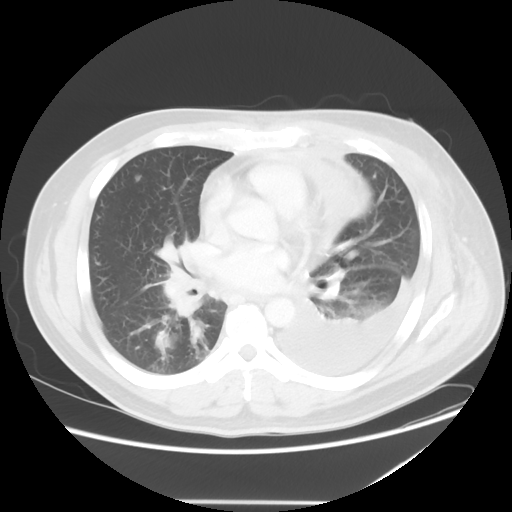
Chest CT, one axial slice. Slice 26 of 52 in the series (ordered by position). Reconstruction kernel STANDARD. 120 kVp. Lung window (W 1500 / L -600 HU). 5 mm slice thickness. 512 × 512 image matrix. Male patient, age 42 years. From the clinical record (not read from this slice): clinical TNM (as recorded): T2 N1 M1.
Annotated regions visible in this slice (rectangle marked by the reading radiologist):
- lung tumour (recorded histology: adenocarcinoma): bounding box <149,327,175,357> (left, top, right, bottom; pixels)